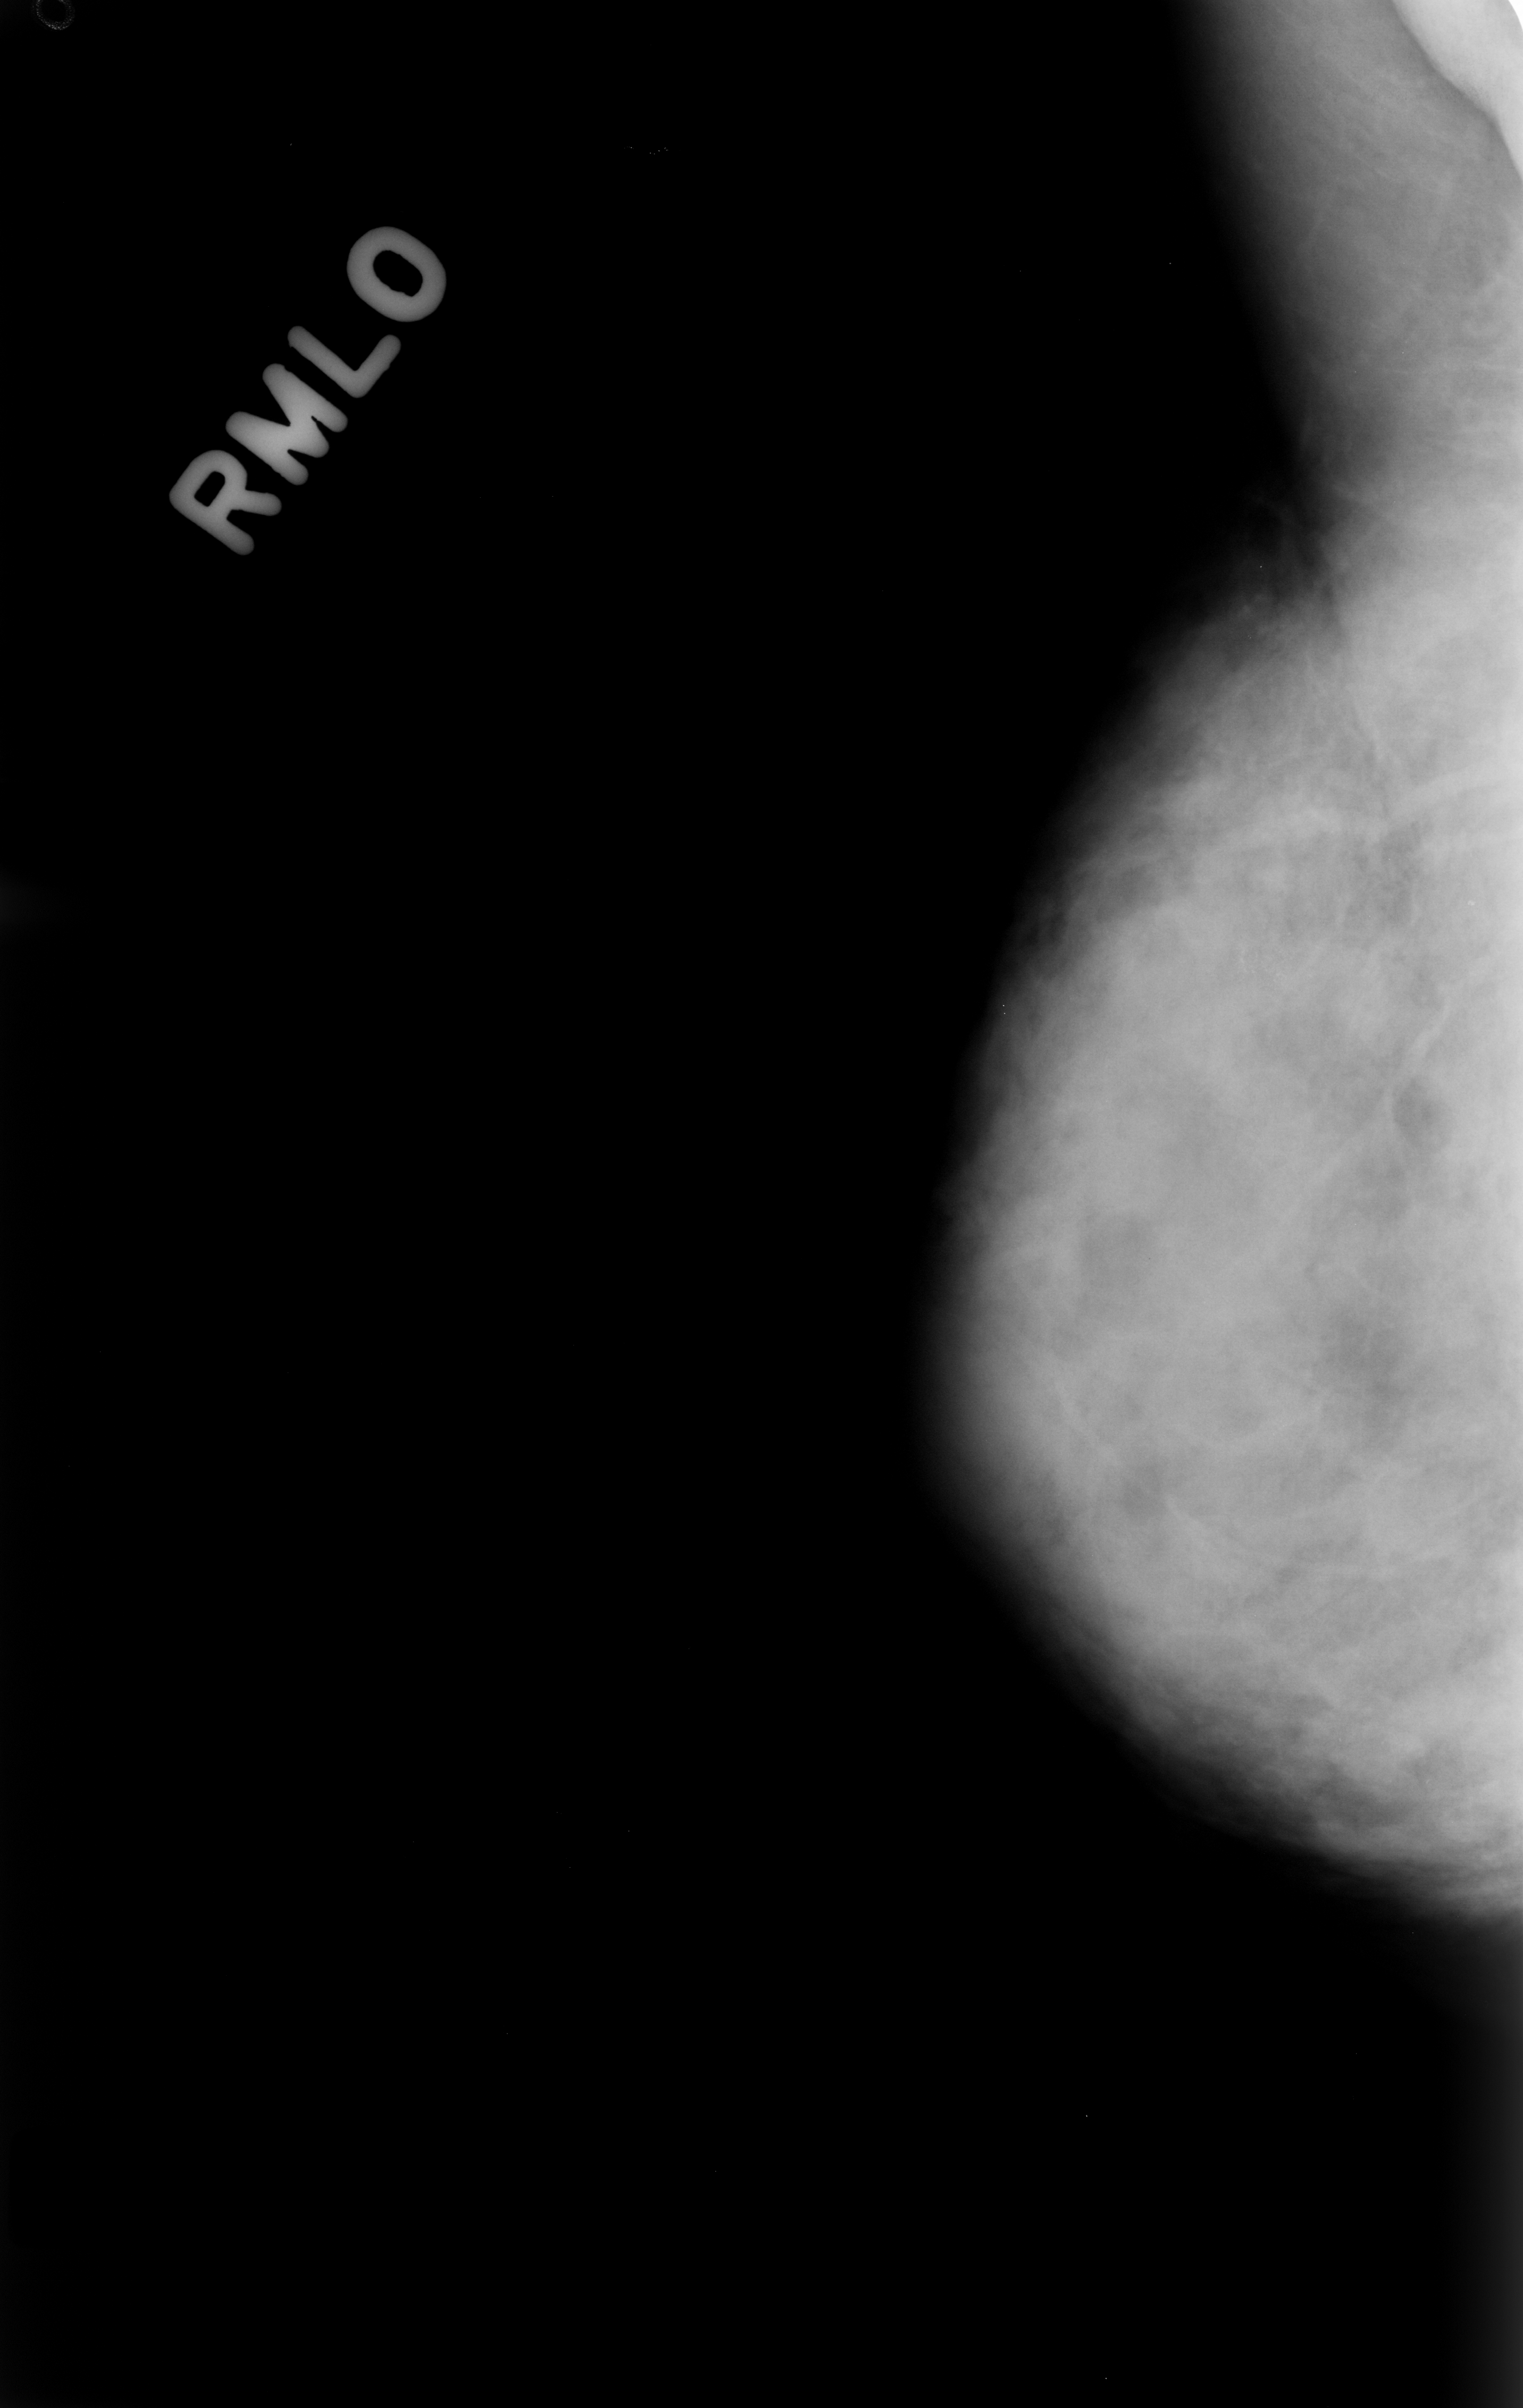
Mammogram (digitized film); right breast; MLO view; BI-RADS breast density category 4 (scale 1–4); 1523 × 2408 image matrix.
Expert-marked regions of interest on this image (one box per marked abnormality):
- calcifications, morphology amorphous, distribution clustered; BI-RADS assessment category 4; subtlety rating 2 on a 1 (subtle) to 5 (obvious) scale; pathology result (as recorded, not read from the image): benign: bounding box [x1, y1, x2, y2] px = [1186, 842, 1388, 1035]